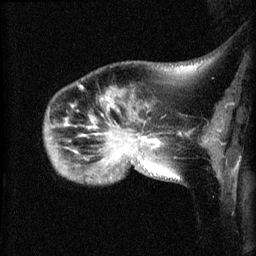
Breast MRI (dynamic contrast-enhanced), one sagittal slice; position 13 of 60 along the scan axis; dynamic contrast-enhanced series, image 2 of 3 at this slice position (ordered by acquisition); 1.5 T; TE 4.2 ms, TR 8.2 ms; 2.1 mm slice thickness; 256 × 256 image matrix, field of view 180 × 180 mm. Patient: female, 50 years.
Outlined on this slice (semi-automatically segmented with operator editing):
- analysis volume of interest (the breast-tissue region the enhancement analysis was run in; not a lesion): bounding box (x1, y1, x2, y2) in pixels: (44, 92, 169, 184)
- tumour enhancement mask (voxels above the 70 % enhancement threshold inside the analysis volume of interest): (116, 139, 160, 159)